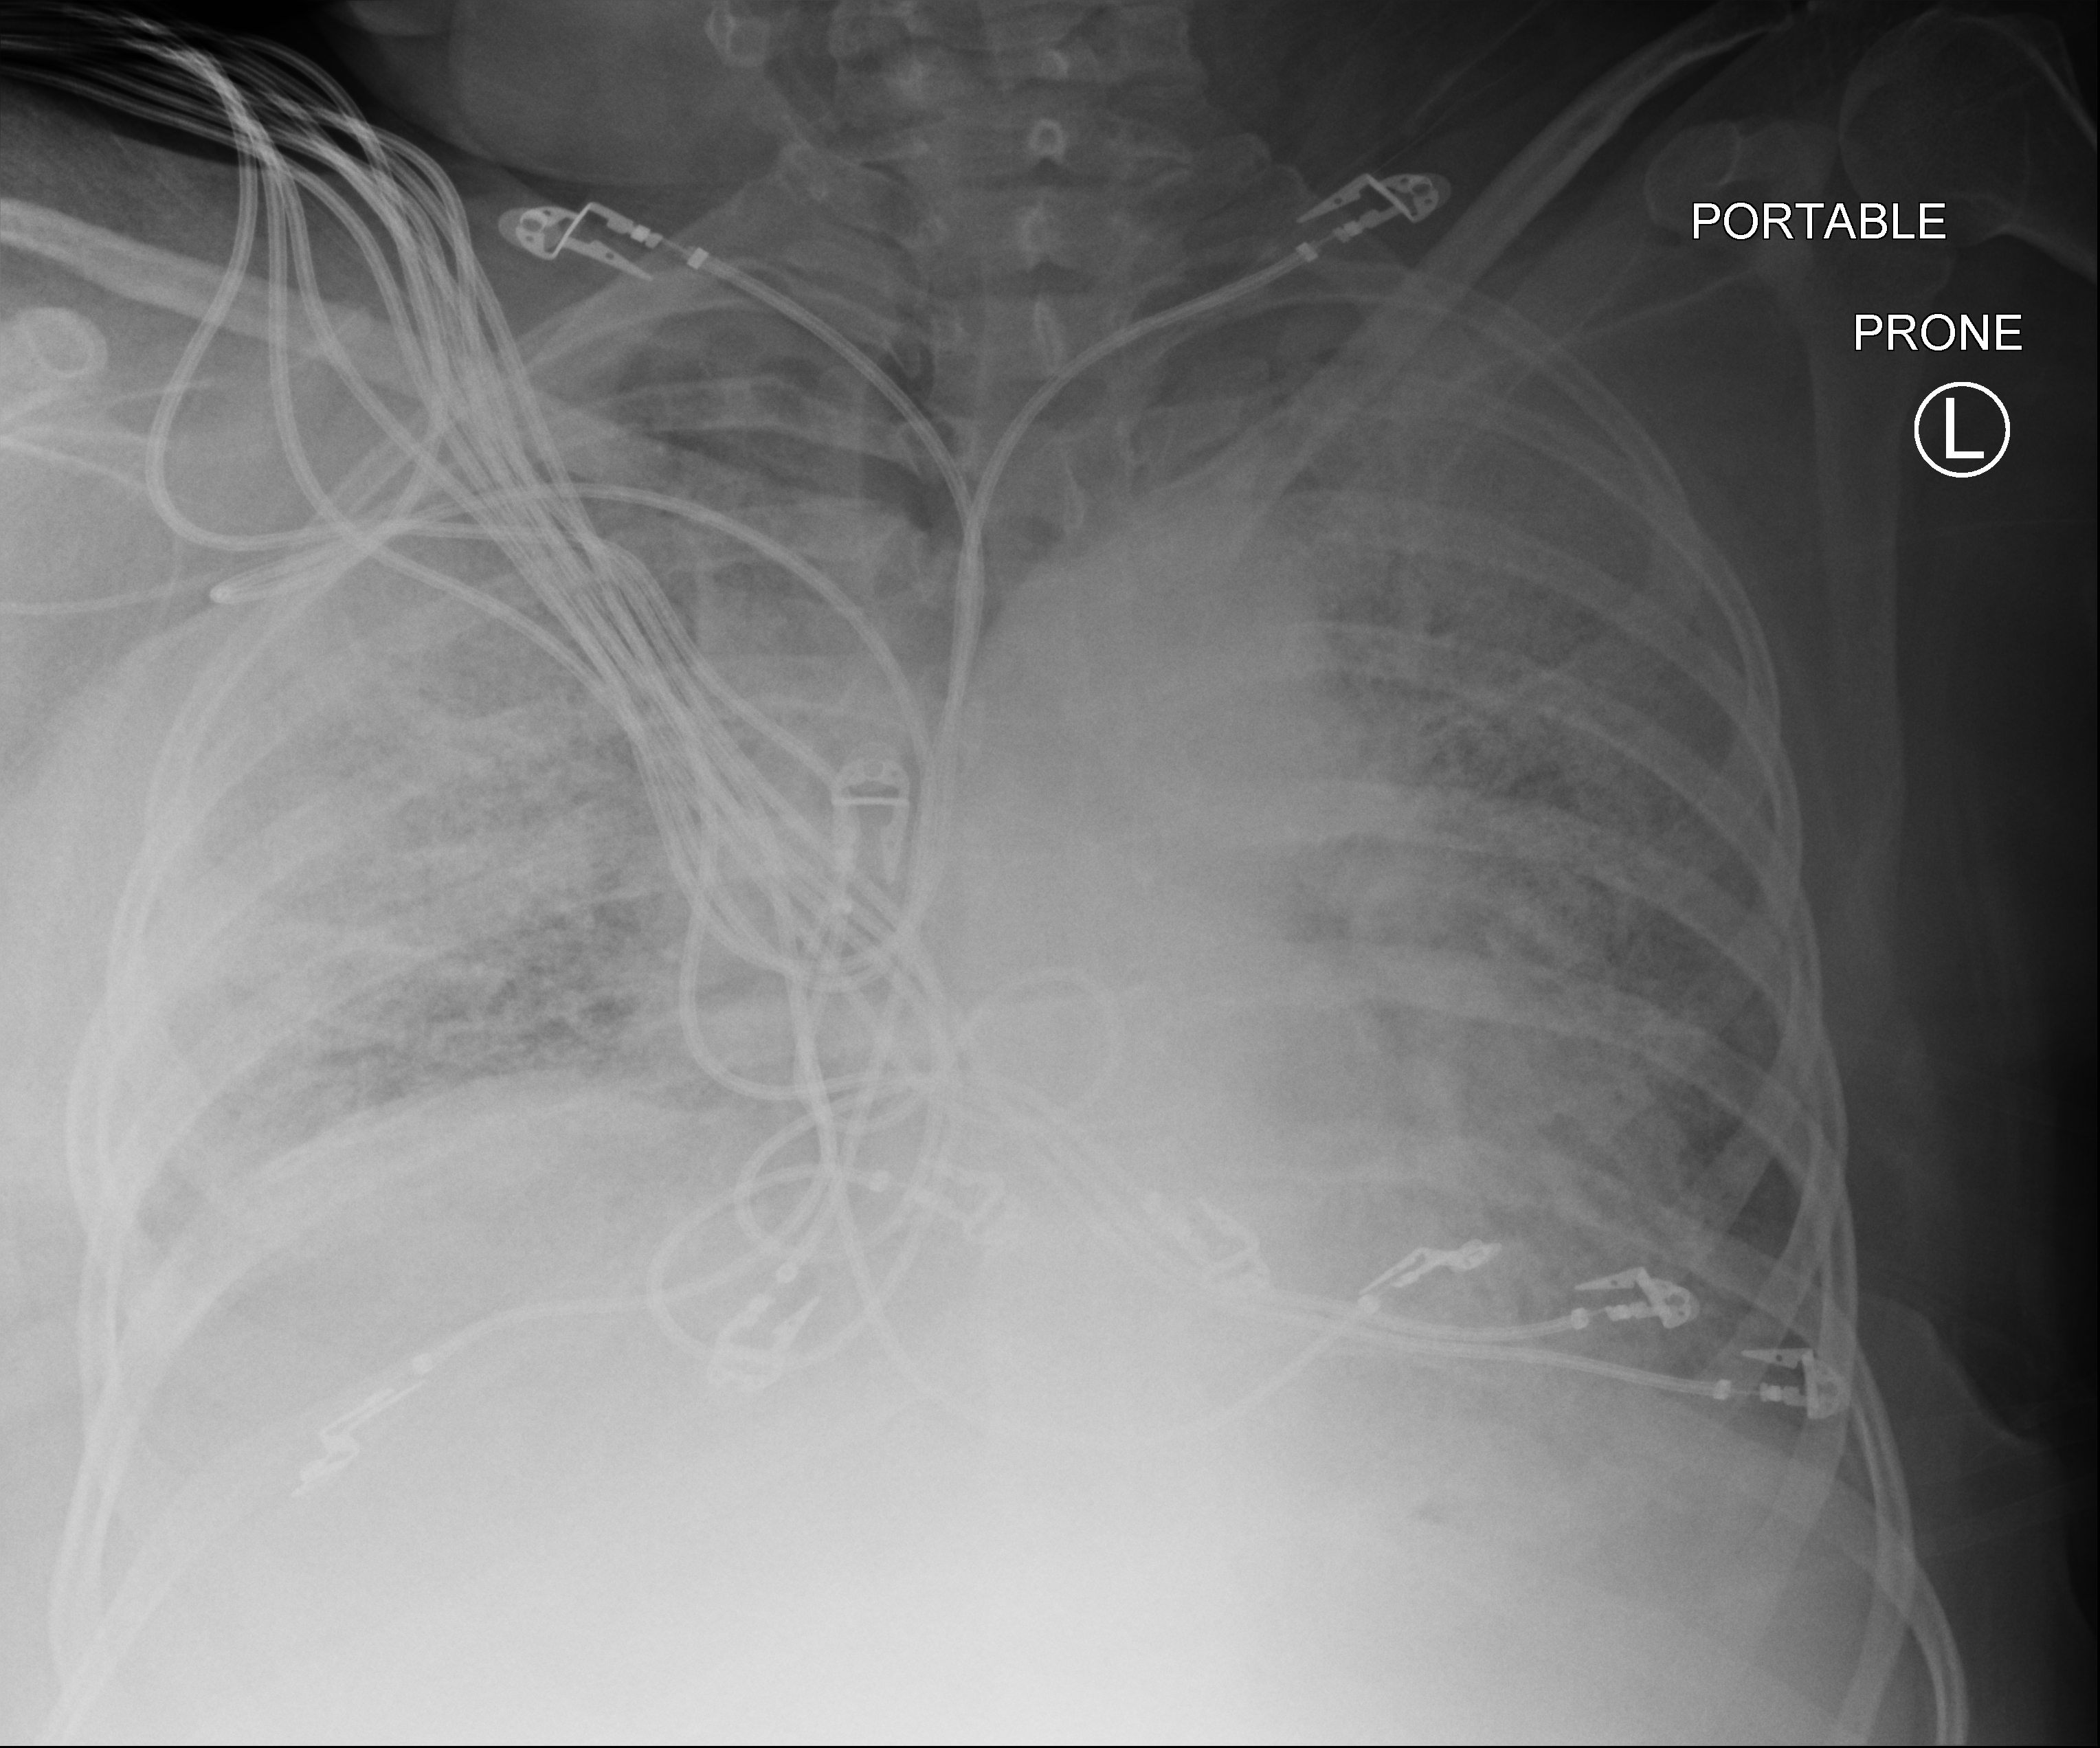
Chest X-ray (portable), anteroposterior (AP) projection. Patient hospitalised with COVID-19; female, aged 18–59 years.
From the hospital-stay record, not from the radiograph (when in the stay this image was taken is not recorded):
- admitted to intensive care during this hospital stay: yes
- hypertension (admission record): no
- diabetes (admission record): no